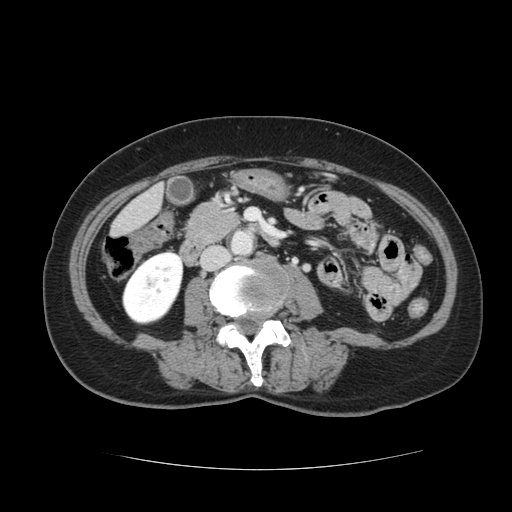
Contrast-enhanced abdominal CT, one axial slice. Slice 19 of 128 in the series (ordered by position). Intravenous contrast given. Soft-tissue window (W 400 / L 40 HU). 2.5 mm slice thickness. 512 × 512 image matrix, field of view 366 × 366 mm. Female patient, age 67 years. From the clinical record (not read from this slice): diagnosis: colorectal cancer liver metastases, imaged before liver resection; multiple liver metastases: yes; largest metastasis: 3 cm; disease in both lobes: yes.
Structures marked on this image (outlined manually by an expert reader):
- liver: bounding box <113,188,162,237> (left, top, right, bottom; pixels)
- planned liver remnant (the part of the liver to remain after resection): <113,206,143,238>